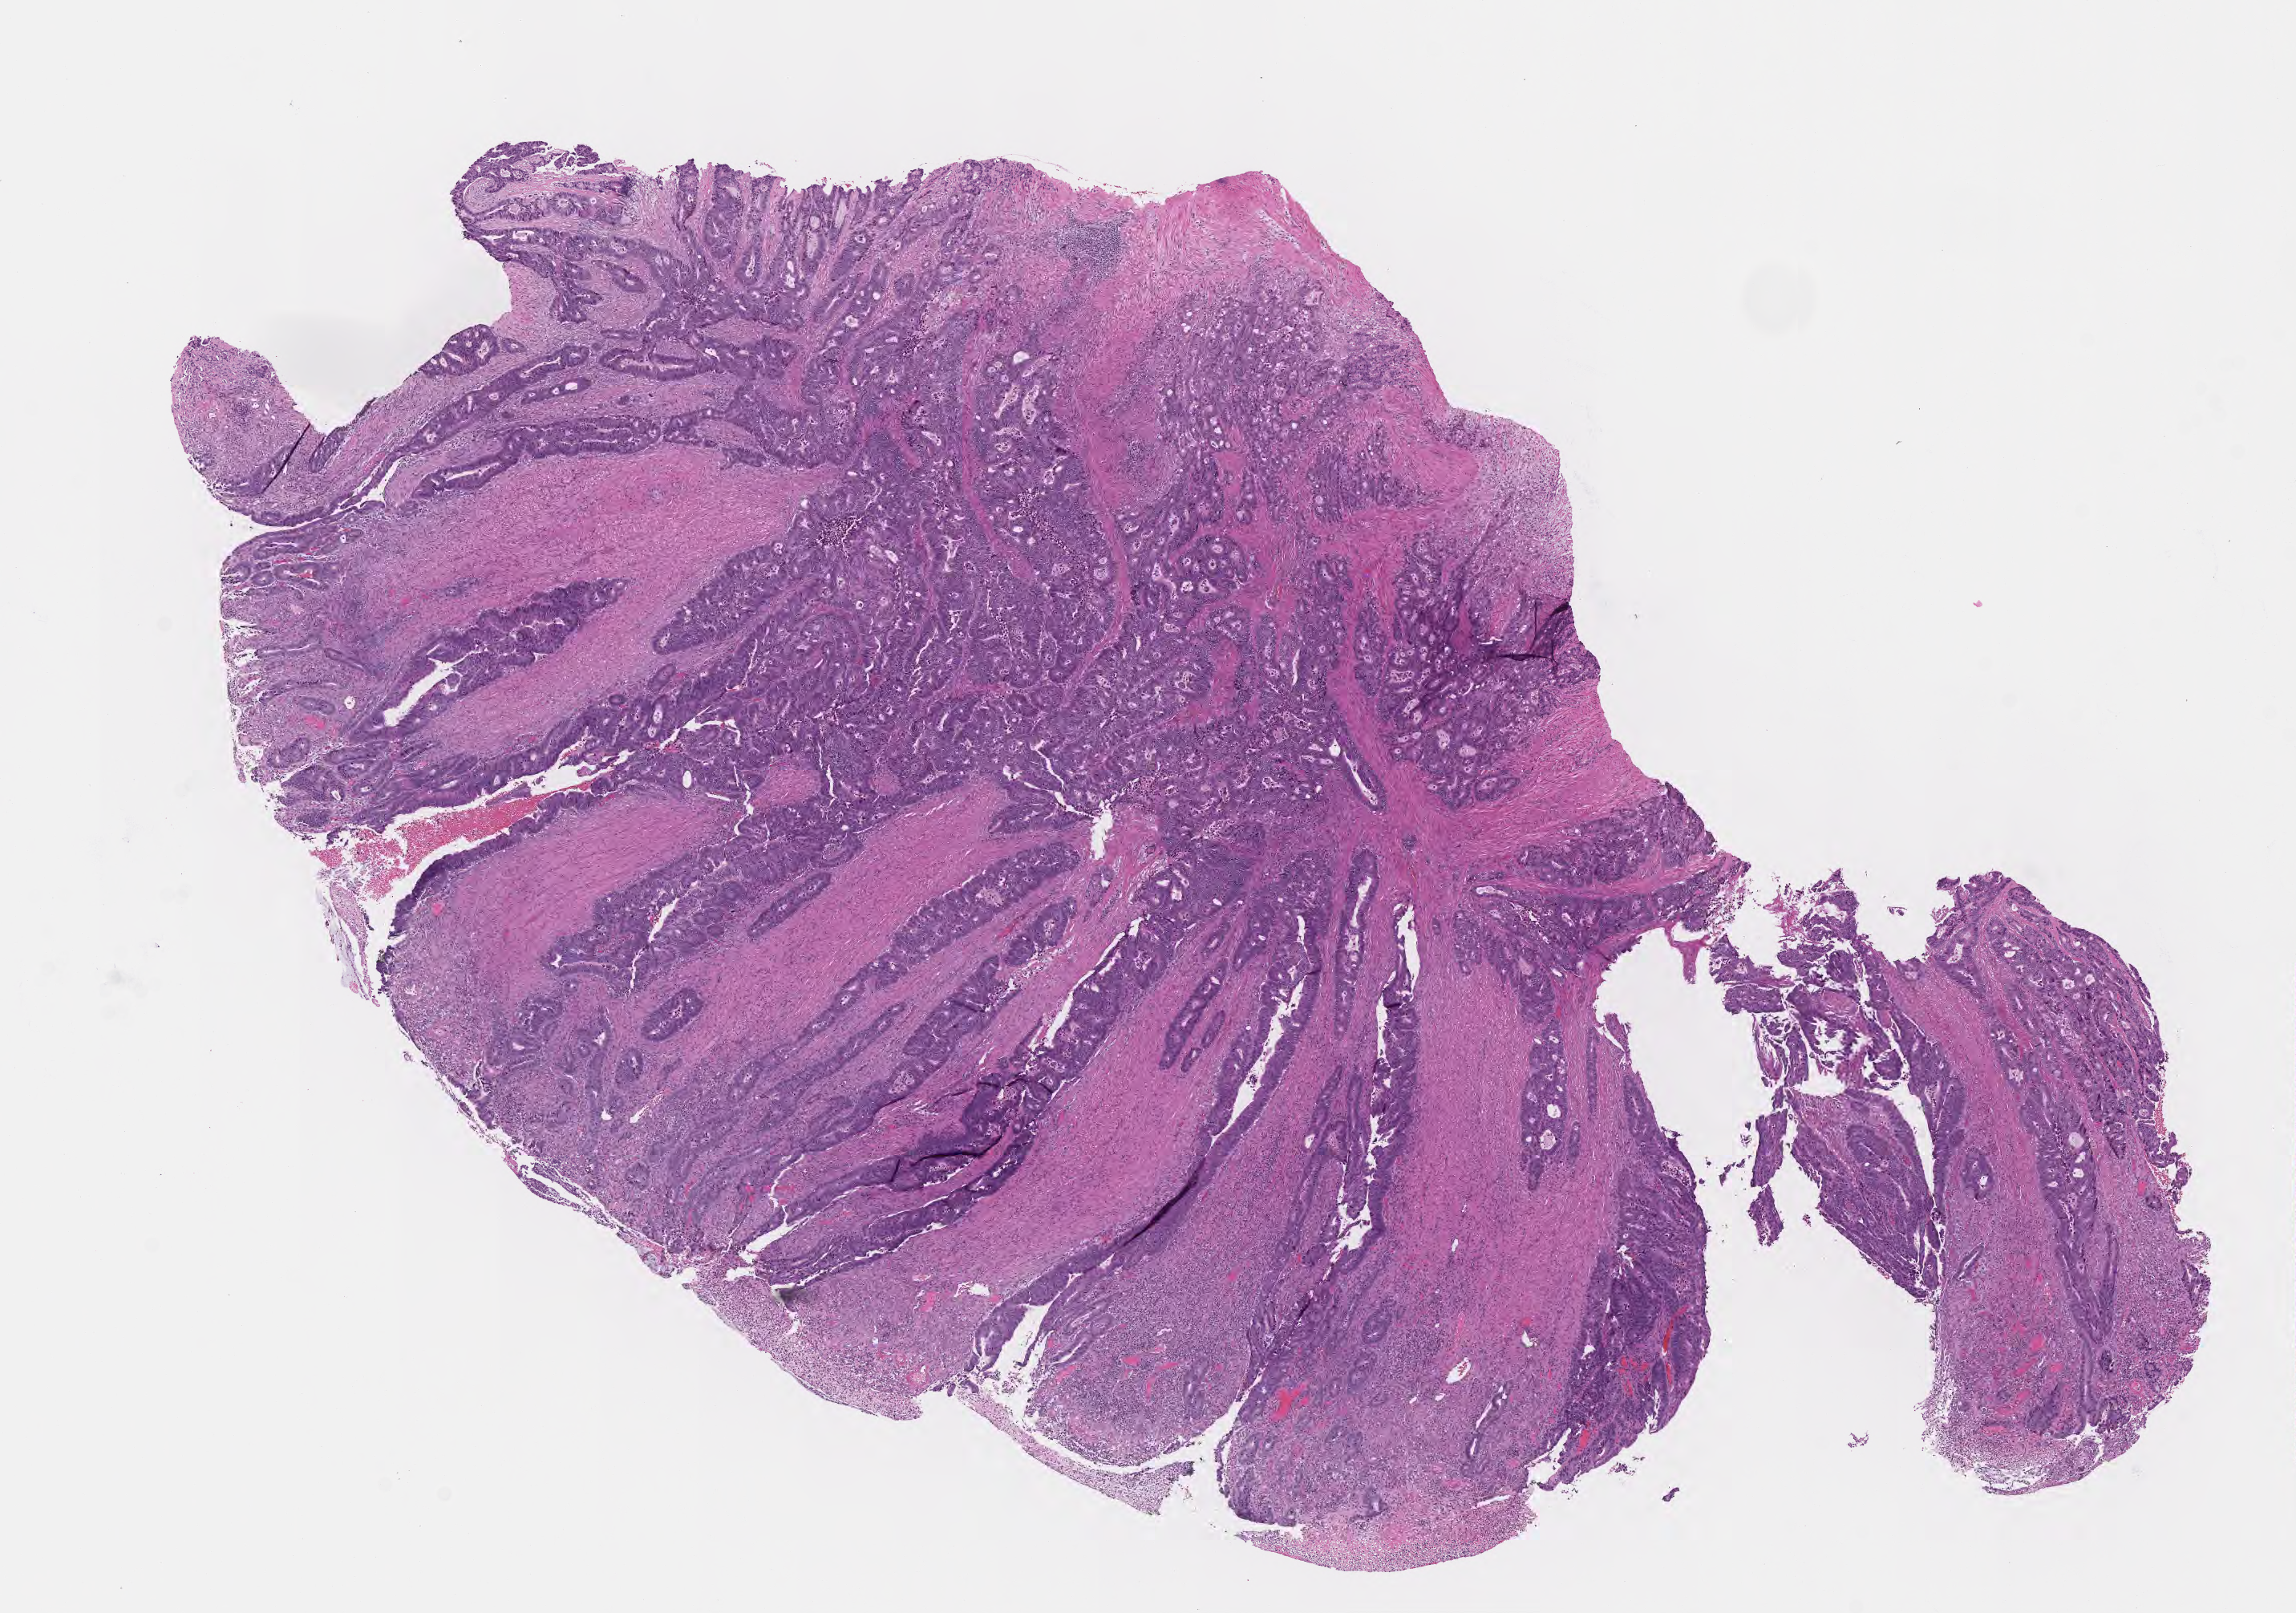
Haematoxylin and eosin whole-slide image — low-resolution overview of the scanned area, about 11.6 x 8.1 mm. Formalin-fixed paraffin-embedded section. Primary tumor. Site: rectosigmoid junction. Female patient; age at initial diagnosis 69 years. Tumor grade: GB (borderline). Slide review estimates, as recorded: tumor cells 95%, tumor nuclei 80%, stromal cells 0%, necrosis 5%, normal cells 0%. Inflammatory infiltration, as recorded: lymphocyte infiltration 0%, monocyte infiltration 0%, neutrophil infiltration 0%.
* AJCC pathologic stage: Stage IIA
* section: bottom of the tissue portion
* histologic diagnosis: Adenocarcinoma, NOS